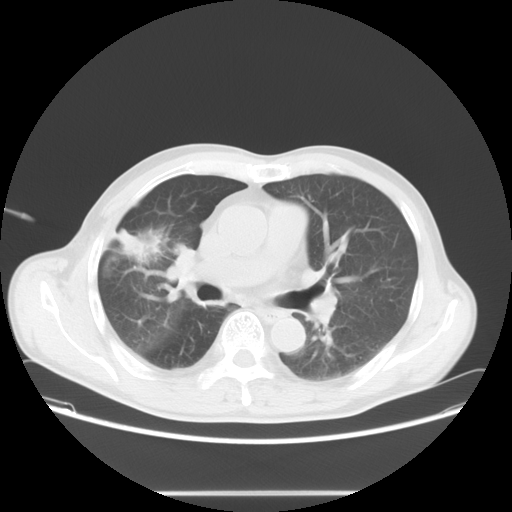
Chest CT, one axial slice. Slice 42 of 69 in the series (ordered by position). Reconstruction kernel STANDARD. Lung window (W 1500 / L -600 HU). 512 × 512 image matrix, field of view 392 × 392 mm. Male patient, age 67 years. Case-level facts recorded for this patient, not image findings: clinical TNM (as recorded): T2 N0 M0.
Outlined on this slice (bounding box drawn by a radiologist):
- lung tumour (recorded histology: adenocarcinoma): bounding box [x1, y1, x2, y2] px = [117, 229, 160, 263]